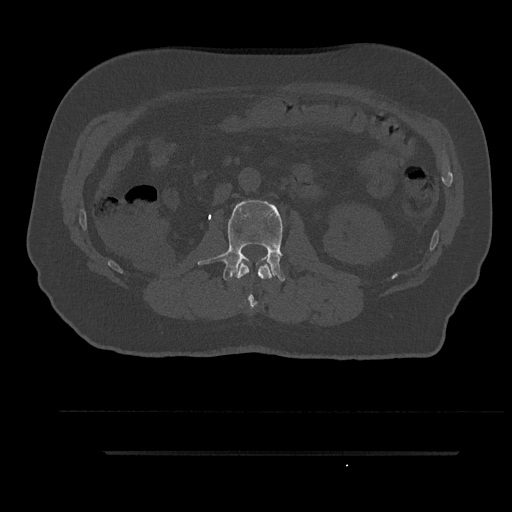
CT including the spine, one axial slice; position 126 of 797 along the scan axis; reconstruction kernel Br40s/3; 120 kVp; bone window (W 1800 / L 400 HU); 0.5 mm slice thickness; 512 × 512 image matrix, field of view 432 × 432 mm. Patient: male, 63 years. Case-level facts recorded for this patient, not image findings: primary cancer: renal; vertebrae with lytic lesions (as recorded): T8.
Outlined on this slice (semi-automatically segmented with operator editing):
- L1 vertebra: bounding box [x1, y1, x2, y2] px = [236, 261, 275, 310]
- L2 vertebra: [198, 200, 285, 281]